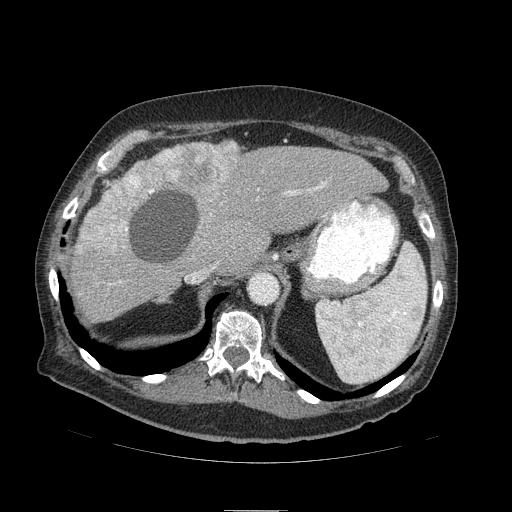
Contrast-enhanced abdominal CT (liver protocol), one axial slice; position 68 of 103 along the scan axis; 120 kVp; soft-tissue window (W 400 / L 40 HU); 2.5 mm slice thickness; 512 × 512 image matrix. Case-level facts recorded for this patient, not image findings: diagnosis: hepatocellular carcinoma (patient treated with transarterial chemoembolisation; whether this scan precedes or follows treatment is not stated here); TNM stage (as recorded): Stage-IIIA; Child-Pugh class: B; tumour differentiation: well differentiated; tumour nodularity: multinodular.
Annotated regions visible in this slice (semi-automatic segmentation, software-assisted and operator-edited):
- liver parenchyma outside the tumour (the mass and vessels are separate outlines, so this box may not span the whole liver): box from (x=70, y=142) to (x=388, y=322) px
- mass: (x=80, y=140)–(x=240, y=256)
- liver vessels: (x=288, y=187)–(x=319, y=195)